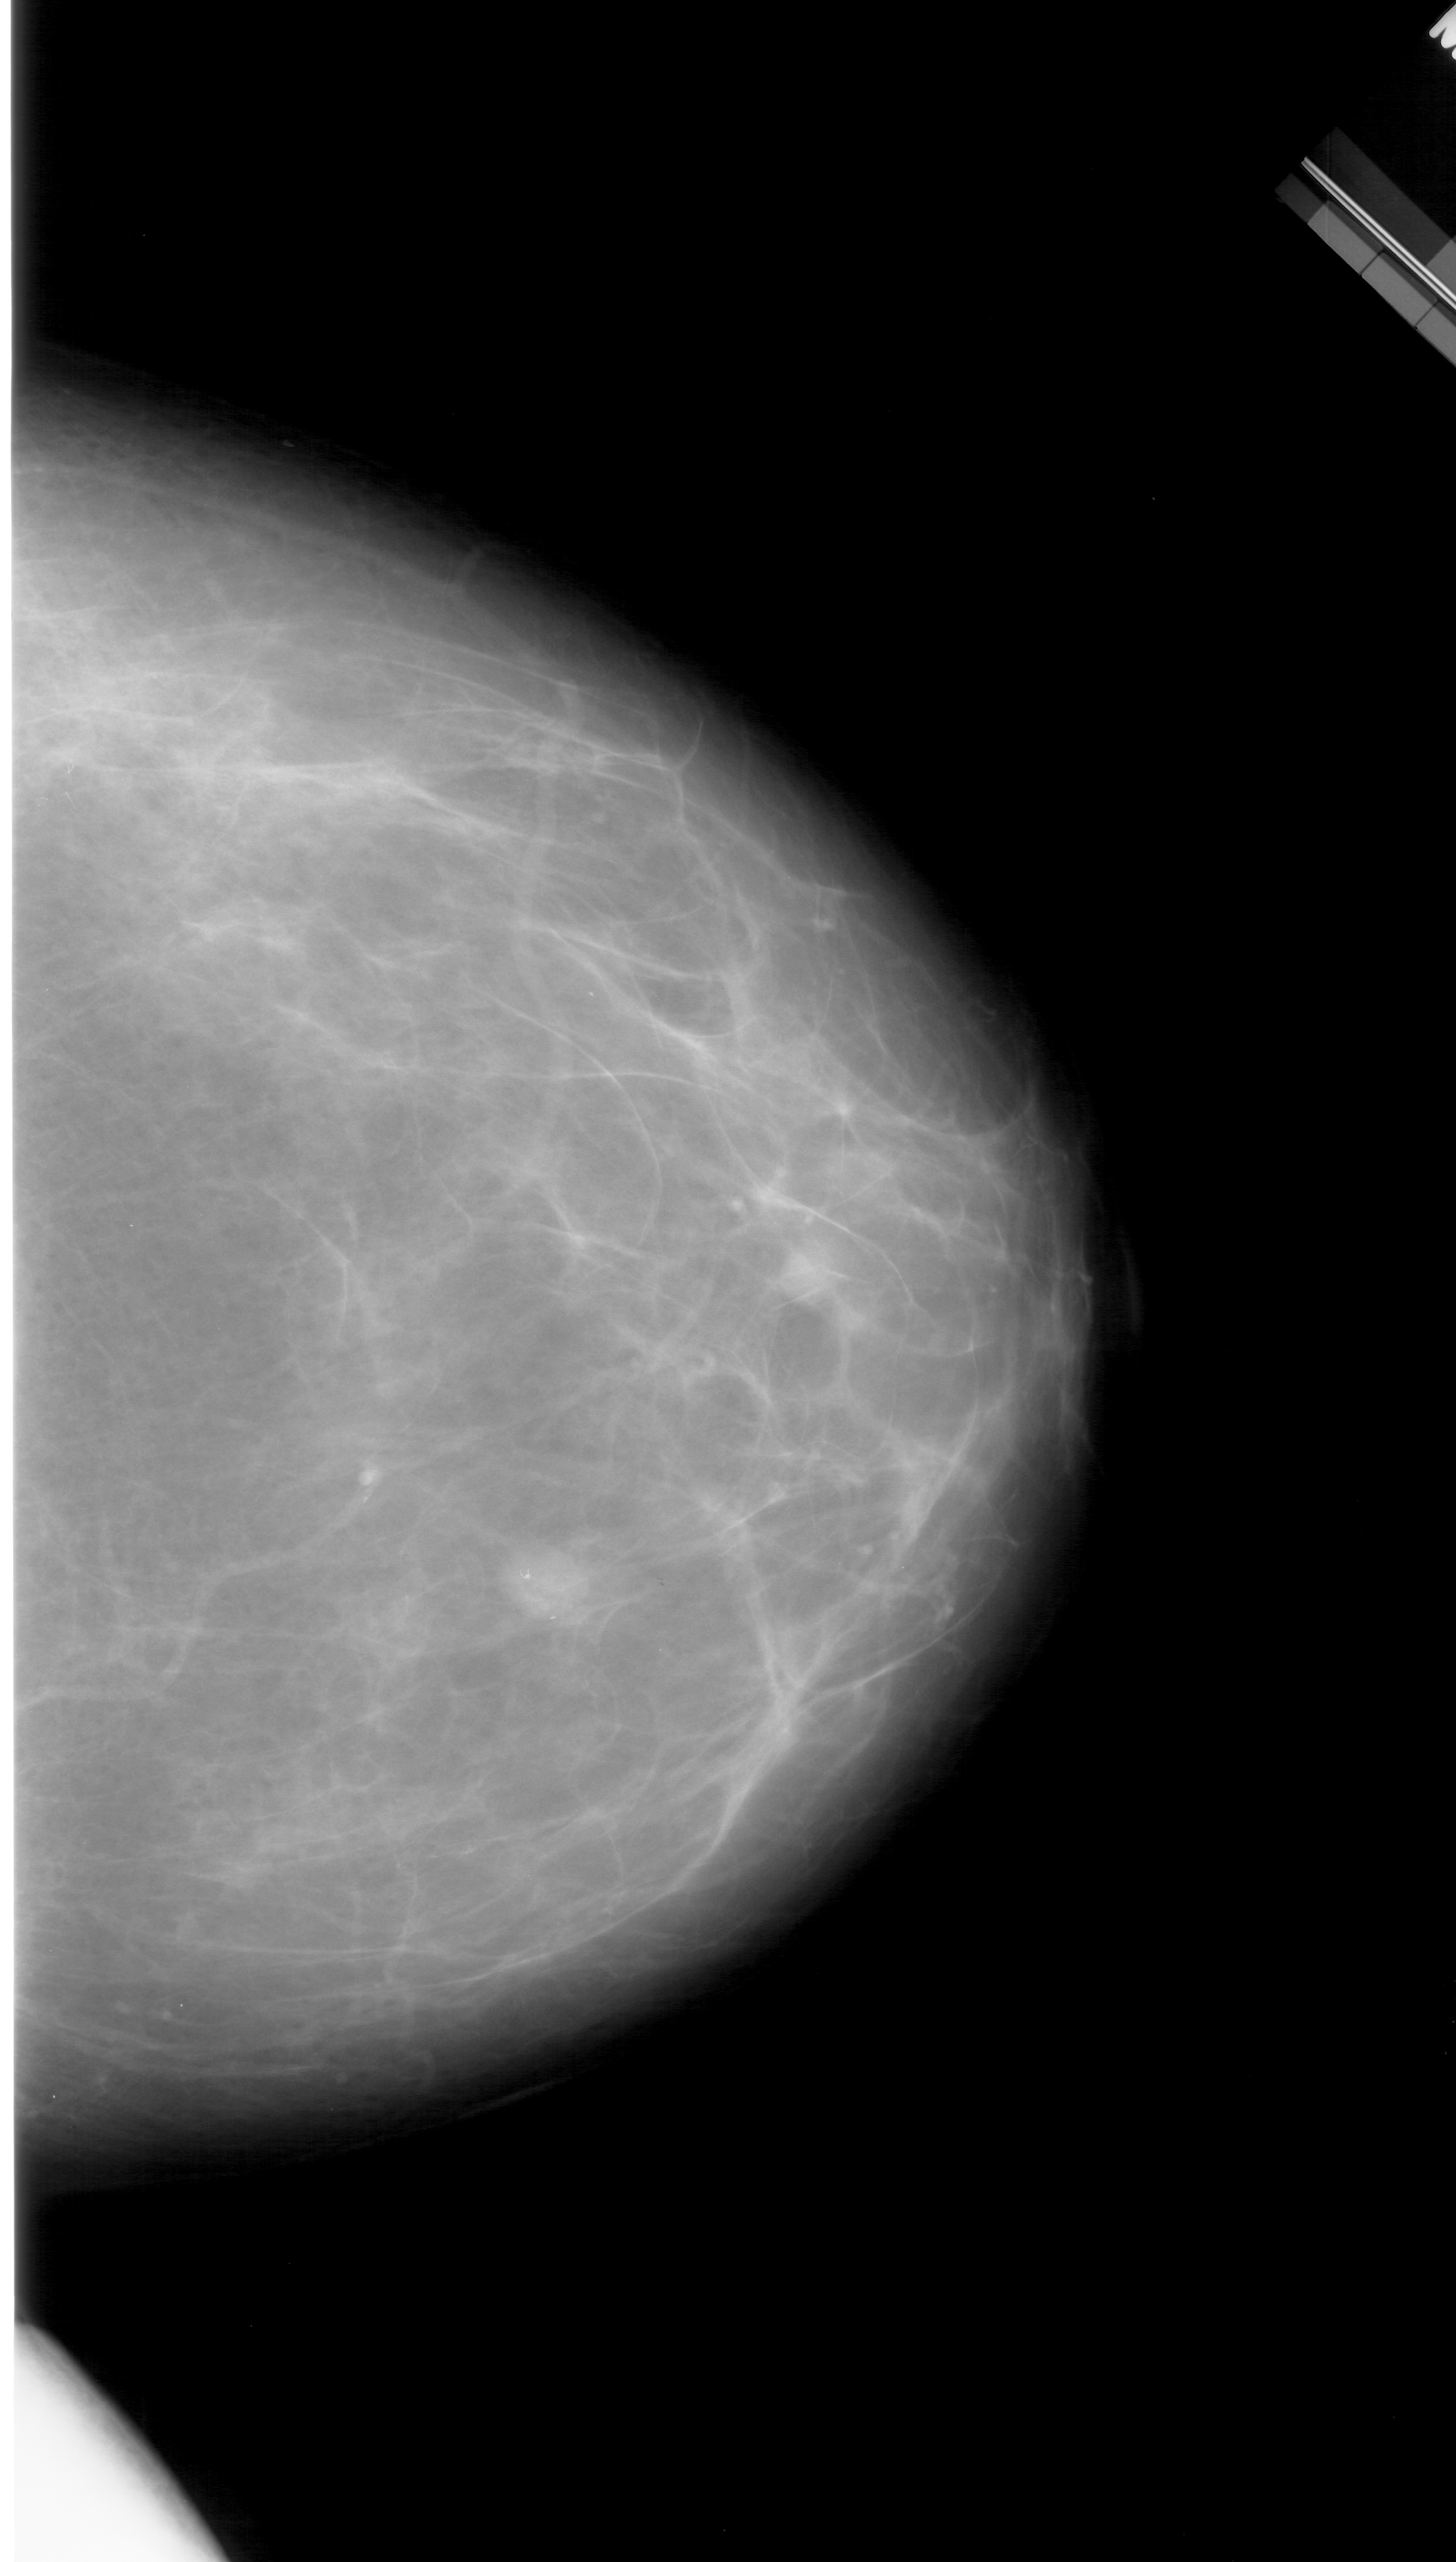
Scanned film-screen mammogram; right breast; CC view; BI-RADS breast density category 2 (scale 1–4); 1456 × 2562 image matrix.
Expert-marked regions of interest on this image (one box per marked abnormality):
- mass, shape oval, margins circumscribed; BI-RADS assessment category 3; pathology result (as recorded, not read from the image): benign: bounding box (x1, y1, x2, y2) in pixels: (493, 1534, 593, 1629)